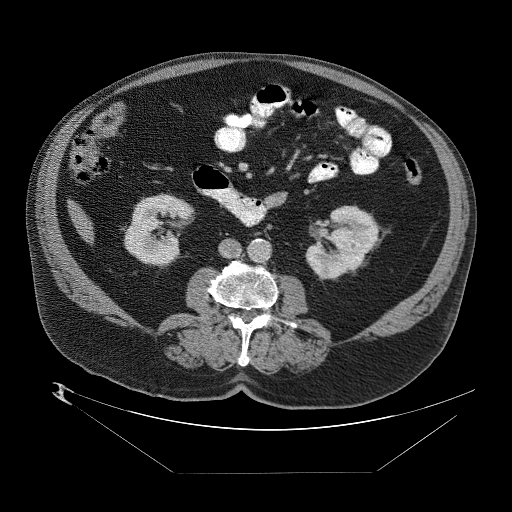
Contrast-enhanced abdominal CT (liver protocol), one axial slice; slice 4 of 89 in the series (ordered by position); reconstruction kernel STANDARD; one of 2 acquisitions stored at this slice position; soft-tissue window (W 400 / L 40 HU); 2.5 mm slice thickness; 512 × 512 image matrix. From the clinical record (not read from this slice): diagnosis: hepatocellular carcinoma (patient treated with transarterial chemoembolisation; whether this scan precedes or follows treatment is not stated here); TNM stage (as recorded): Stage-II; Child-Pugh class: B.
Annotated regions visible in this slice (semi-automatic segmentation, software-assisted and operator-edited):
- abdominal aorta: box from (x=248, y=239) to (x=271, y=263) px
- liver parenchyma outside the tumour (the mass and vessels are separate outlines, so this box may not span the whole liver): (x=66, y=195)–(x=92, y=239)